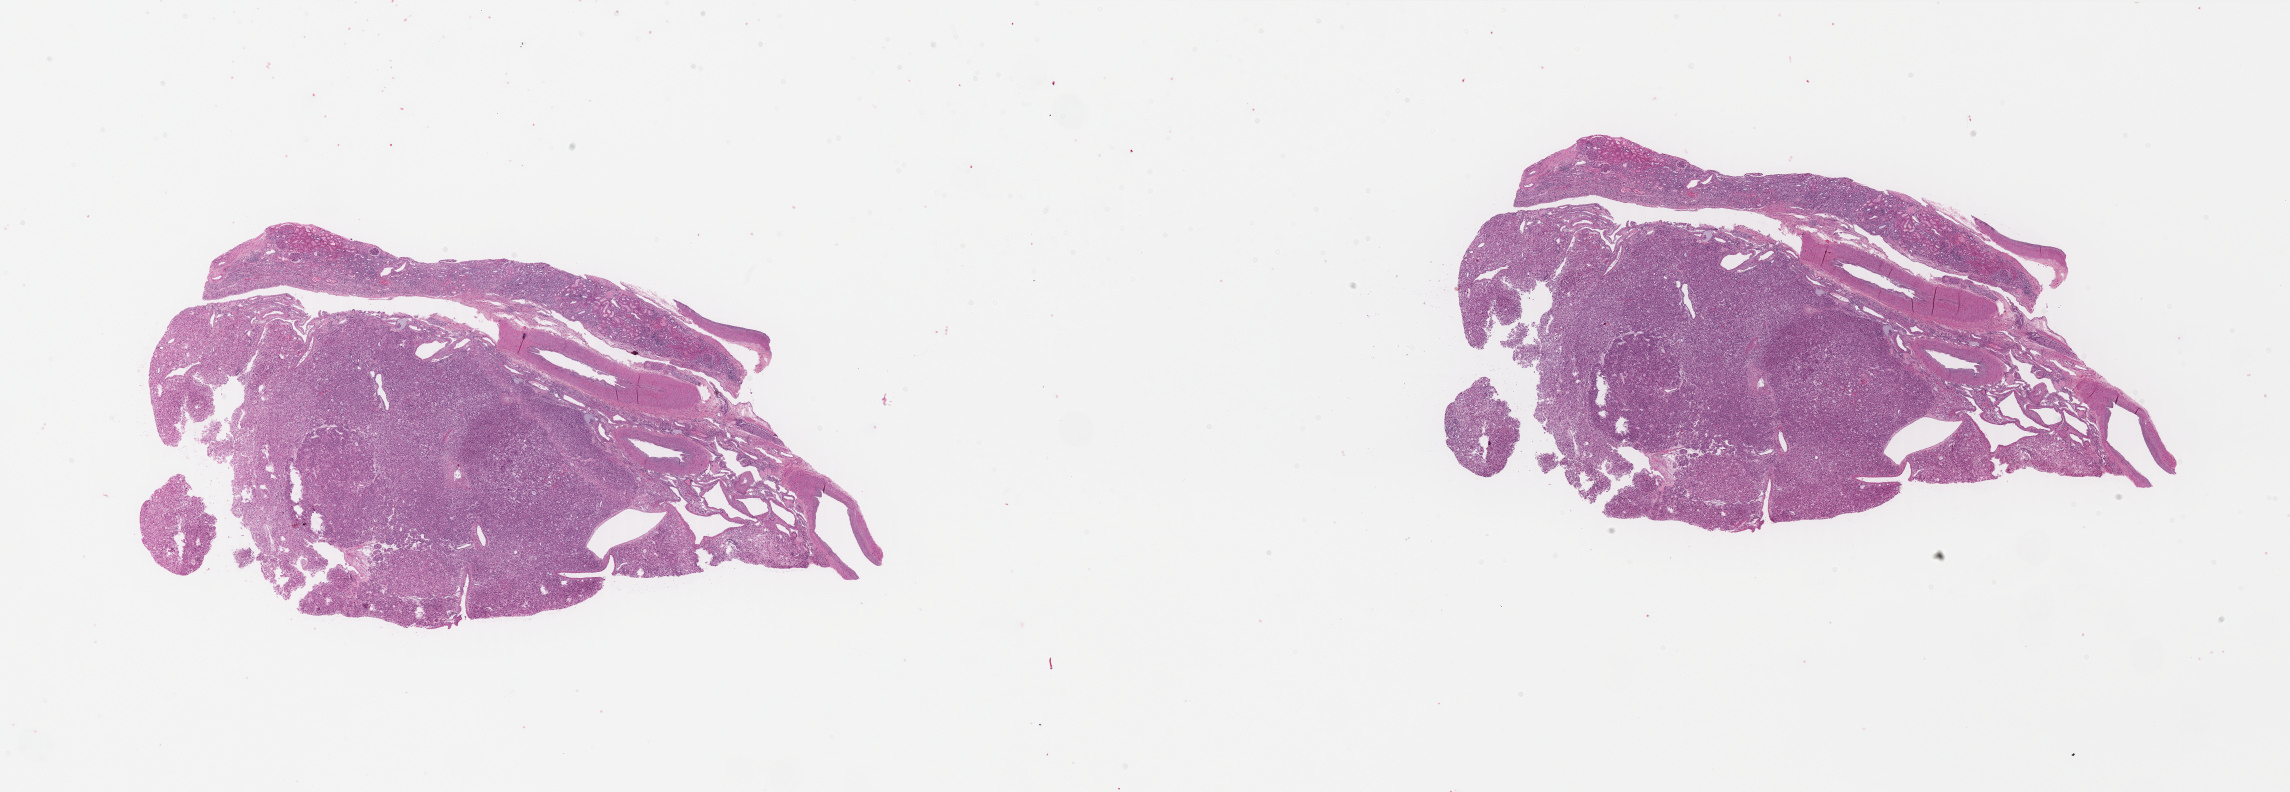
Whole-slide histology image, Hematoxylin and eosin (H&E) stained, low-resolution overview of the scanned area, about 36.2 x 12.5 mm, formalin-fixed paraffin-embedded (FFPE) diagnostic section, primary tumour sample from the kidney. Female patient; age at initial diagnosis 75 years. Composition of this section per pathologist review: tumour cells 70%, tumour nuclei 70%, normal cells 10%, stromal cells 20%, necrosis 0%. Inflammatory infiltration, as recorded: lymphocyte infiltration 3%, monocyte infiltration 1%, neutrophil infiltration 1%.
* AJCC pathologic stage: I (7th edition)
* histologic diagnosis: Renal cell carcinoma, chromophobe type
* laterality: right
* lymph nodes positive (case pathology): 0 of 1 examined